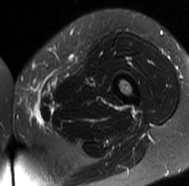
MRI of an extremity soft-tissue mass, one axial slice. Slice 17 of 77 in the series (ordered by position). T2-weighted fat-saturated. MR volume resampled by the dataset authors to the PET/CT grid (not the native acquisition matrix). 3.27 mm slice thickness. 189 × 186 image matrix, field of view 185 × 182 mm. Female patient. From the clinical record (not read from this slice): histological type: leiomyosarcoma; grade: high; site of the primary tumour: groin.
Annotated regions visible in this slice (expert contour drawn on MRI and transferred to this co-registered scan by the dataset authors):
- gross tumour volume including surrounding oedema: box from (x=15, y=97) to (x=43, y=123) px